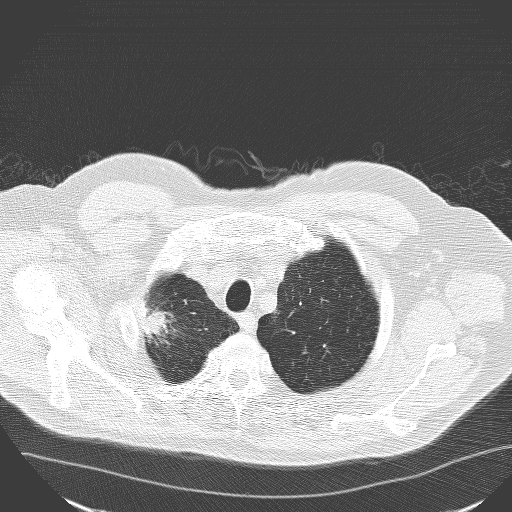
Axial slice from a low-dose chest CT screening exam, baseline screening round, lung window (W 1500 / L -600 HU), 3.2 mm slice thickness, lung (sharp) reconstruction kernel (D), 512 × 512 image matrix. Male participant, aged 71 years at enrolment. Current smoker at enrolment.
Lesion marked by an expert reader, bounding box <118,289,189,362> (left, top, right, bottom; pixels). The exam's reader record, not a measurement of the box and not confirmed to be the same lesion: non-calcified nodule or mass ≥4 mm, right upper lobe, 30 × 25 mm, spiculated (stellate) margins, soft tissue attenuation. Participant outcome: lung cancer diagnosed 182 days after this screen — squamous cell carcinoma, NOS, right upper lobe, poorly differentiated (G3), stage IA (AJCC 6th edition), 30 mm at pathology.